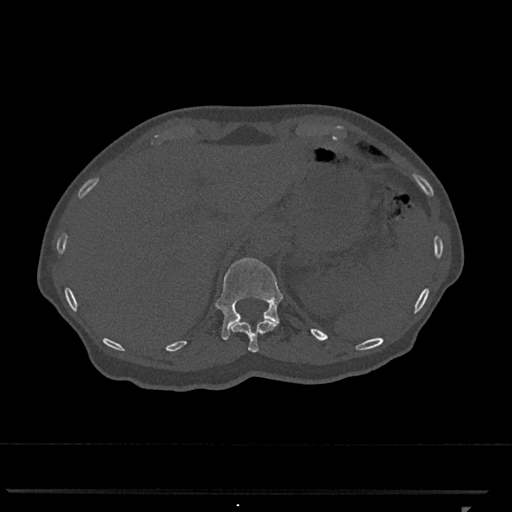
CT including the spine, one axial slice. Slice 486 of 793 in the series (ordered by position). 120 kVp. Bone window (W 1800 / L 400 HU). 512 × 512 image matrix, field of view 380 × 380 mm. Female patient, age 62 years. From the clinical record (not read from this slice): primary cancer: renal.
Outlined on this slice (semi-automatically segmented with operator editing):
- T11 vertebra: bounding box (x1, y1, x2, y2) in pixels: (231, 319, 277, 352)
- T12 vertebra: (215, 258, 283, 340)